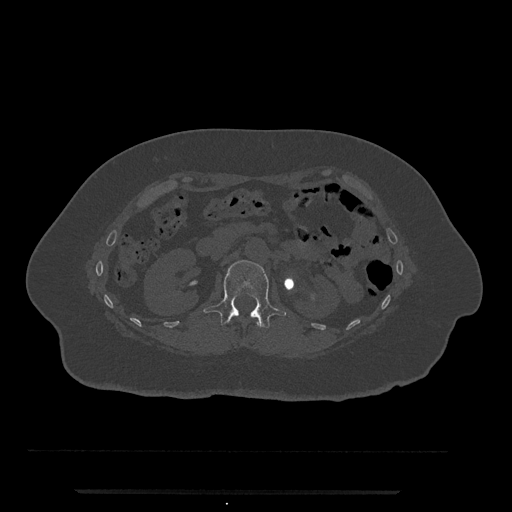
CT including the spine, one axial slice; slice 111 of 797 in the series (ordered by position); bone window (W 1800 / L 400 HU); 0.5 mm slice thickness; 512 × 512 image matrix, field of view 440 × 440 mm. Female patient, age 51 years. Case-level facts recorded for this patient, not image findings: primary cancer: neuro; vertebrae with lytic lesions (as recorded): T8.
Annotated regions visible in this slice (semi-automatic segmentation, software-assisted and operator-edited):
- L1 vertebra: box from (x=203, y=260) to (x=286, y=329) px
- T12 vertebra: (x=256, y=322)–(x=260, y=327)